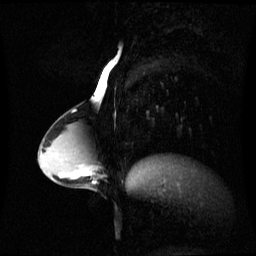
Breast MRI (dynamic contrast-enhanced), one sagittal slice. Position 31 of 60 along the scan axis. Dynamic contrast-enhanced series, image 2 of 3 at this slice position (ordered by acquisition). 1.5 T. TE 4.2 ms, TR 8.4 ms. 256 × 256 image matrix, field of view 280 × 280 mm. Patient: female, 34 years. From the clinical record (not read from this slice): setting: breast cancer imaged before/during neoadjuvant chemotherapy; receptor status: triple-negative.
Structures marked on this image (semi-automatic segmentation, software-assisted and operator-edited):
- analysis volume of interest (the breast-tissue region the enhancement analysis was run in; not a lesion): bounding box (x1, y1, x2, y2) in pixels: (57, 156, 96, 189)
- tumour enhancement mask (voxels above the 70 % enhancement threshold inside the analysis volume of interest): (85, 172, 91, 175)